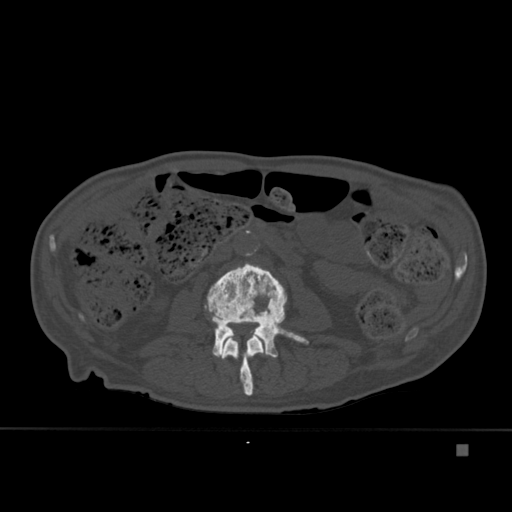
CT including the spine, one axial slice; position 149 of 451 along the scan axis; bone window (W 1800 / L 400 HU); 512 × 512 image matrix, field of view 378 × 378 mm. Patient: male, 75 years. From the clinical record (not read from this slice): primary cancer: prostate.
Outlined on this slice (semi-automatically segmented with operator editing):
- L2 vertebra: bounding box <221,335,265,396> (left, top, right, bottom; pixels)
- L3 vertebra: <204,263,309,358>